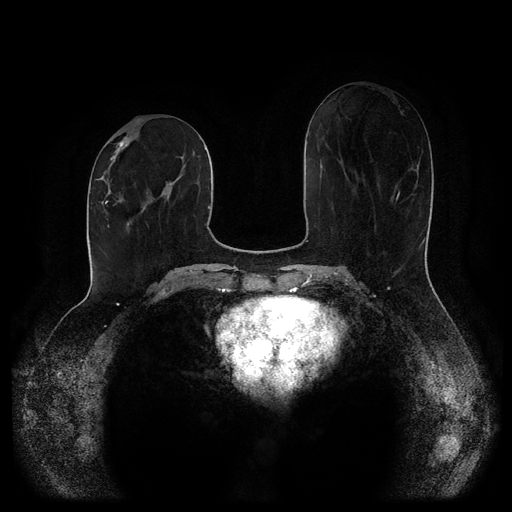
Breast MRI (dynamic contrast-enhanced, multi-phase), one axial slice; slice 43 of 116 in the series (ordered by position); dynamic contrast-enhanced series, time point 2 of 5 at this slice position (early post-contrast); 1.5 T; TE 2.6 ms, TR 5.2 ms; 2 mm slice thickness; 512 × 512 image matrix, field of view 380 × 380 mm. Patient: female, 52 years.
Annotated regions visible in this slice (semi-automatic segmentation, software-assisted and operator-edited):
- breast lesion (labelled 'tumour' in the annotation; benign lesions carry a separate 'benign' label): bounding box [x1, y1, x2, y2] px = [97, 136, 130, 184]